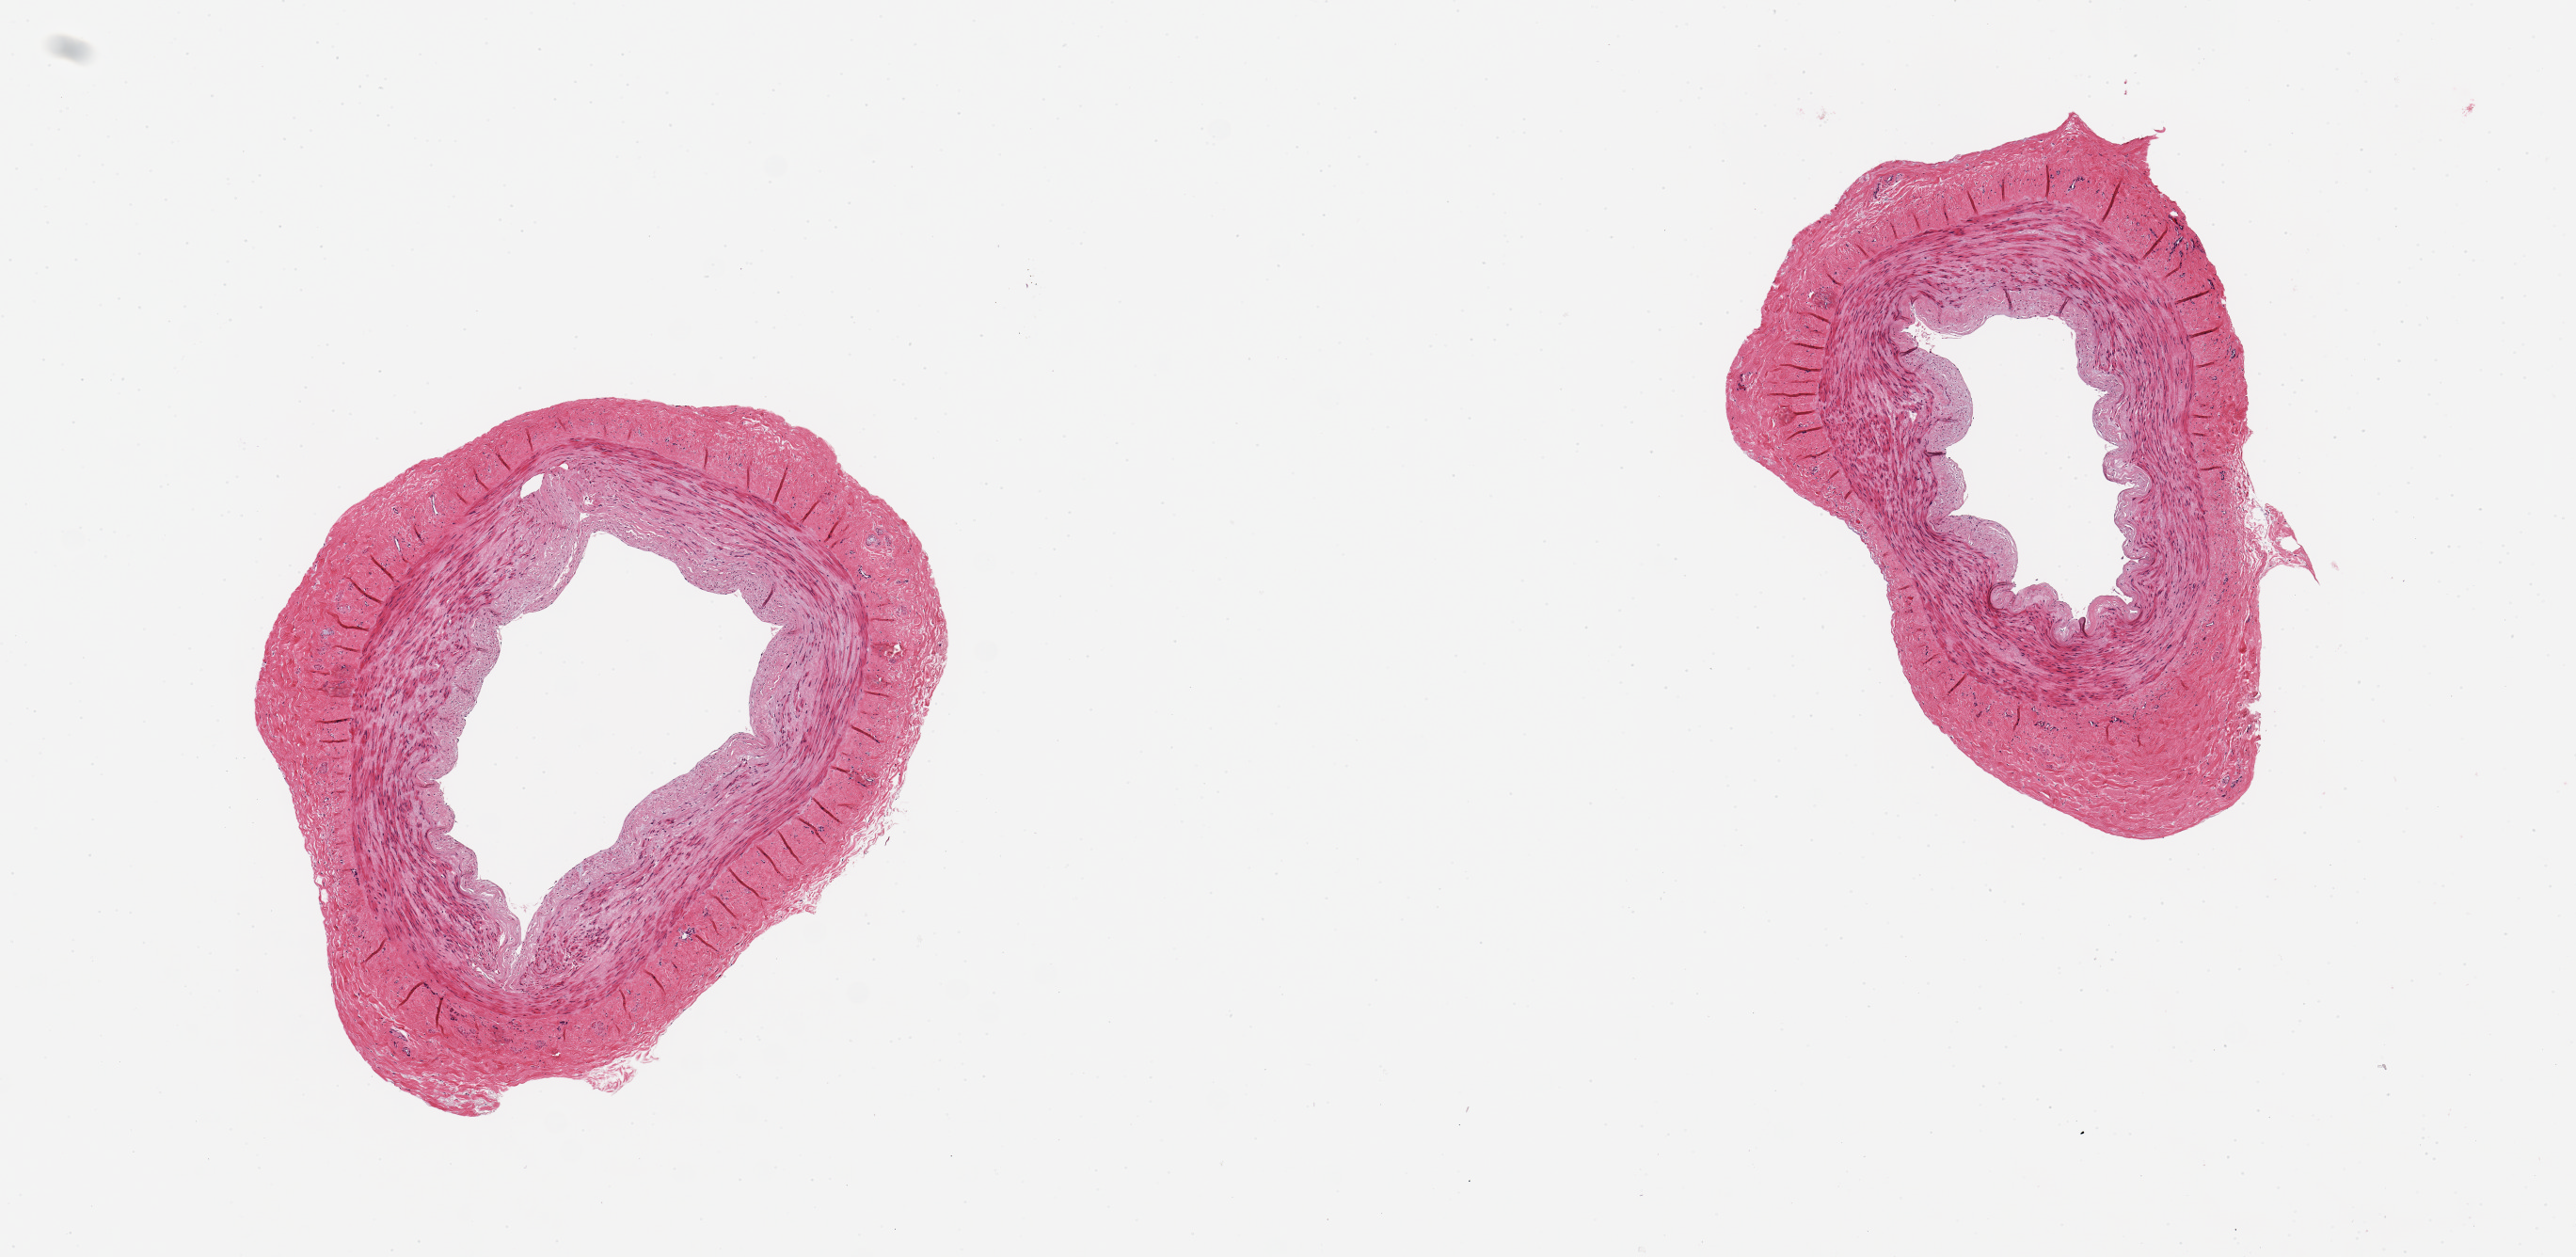
Digitized haematoxylin and eosin-stained section — whole scanned area (about 10.8 x 5.3 mm, acquisition: 20x scan) shown as a low-resolution overview, PAXgene-fixed paraffin-embedded (PFPE) section, sampled site (target tissue): tibial artery, tissue donor sample. Donor: male.
Review note (as recorded): 2 ~3mm d aliquots, clean specimens.